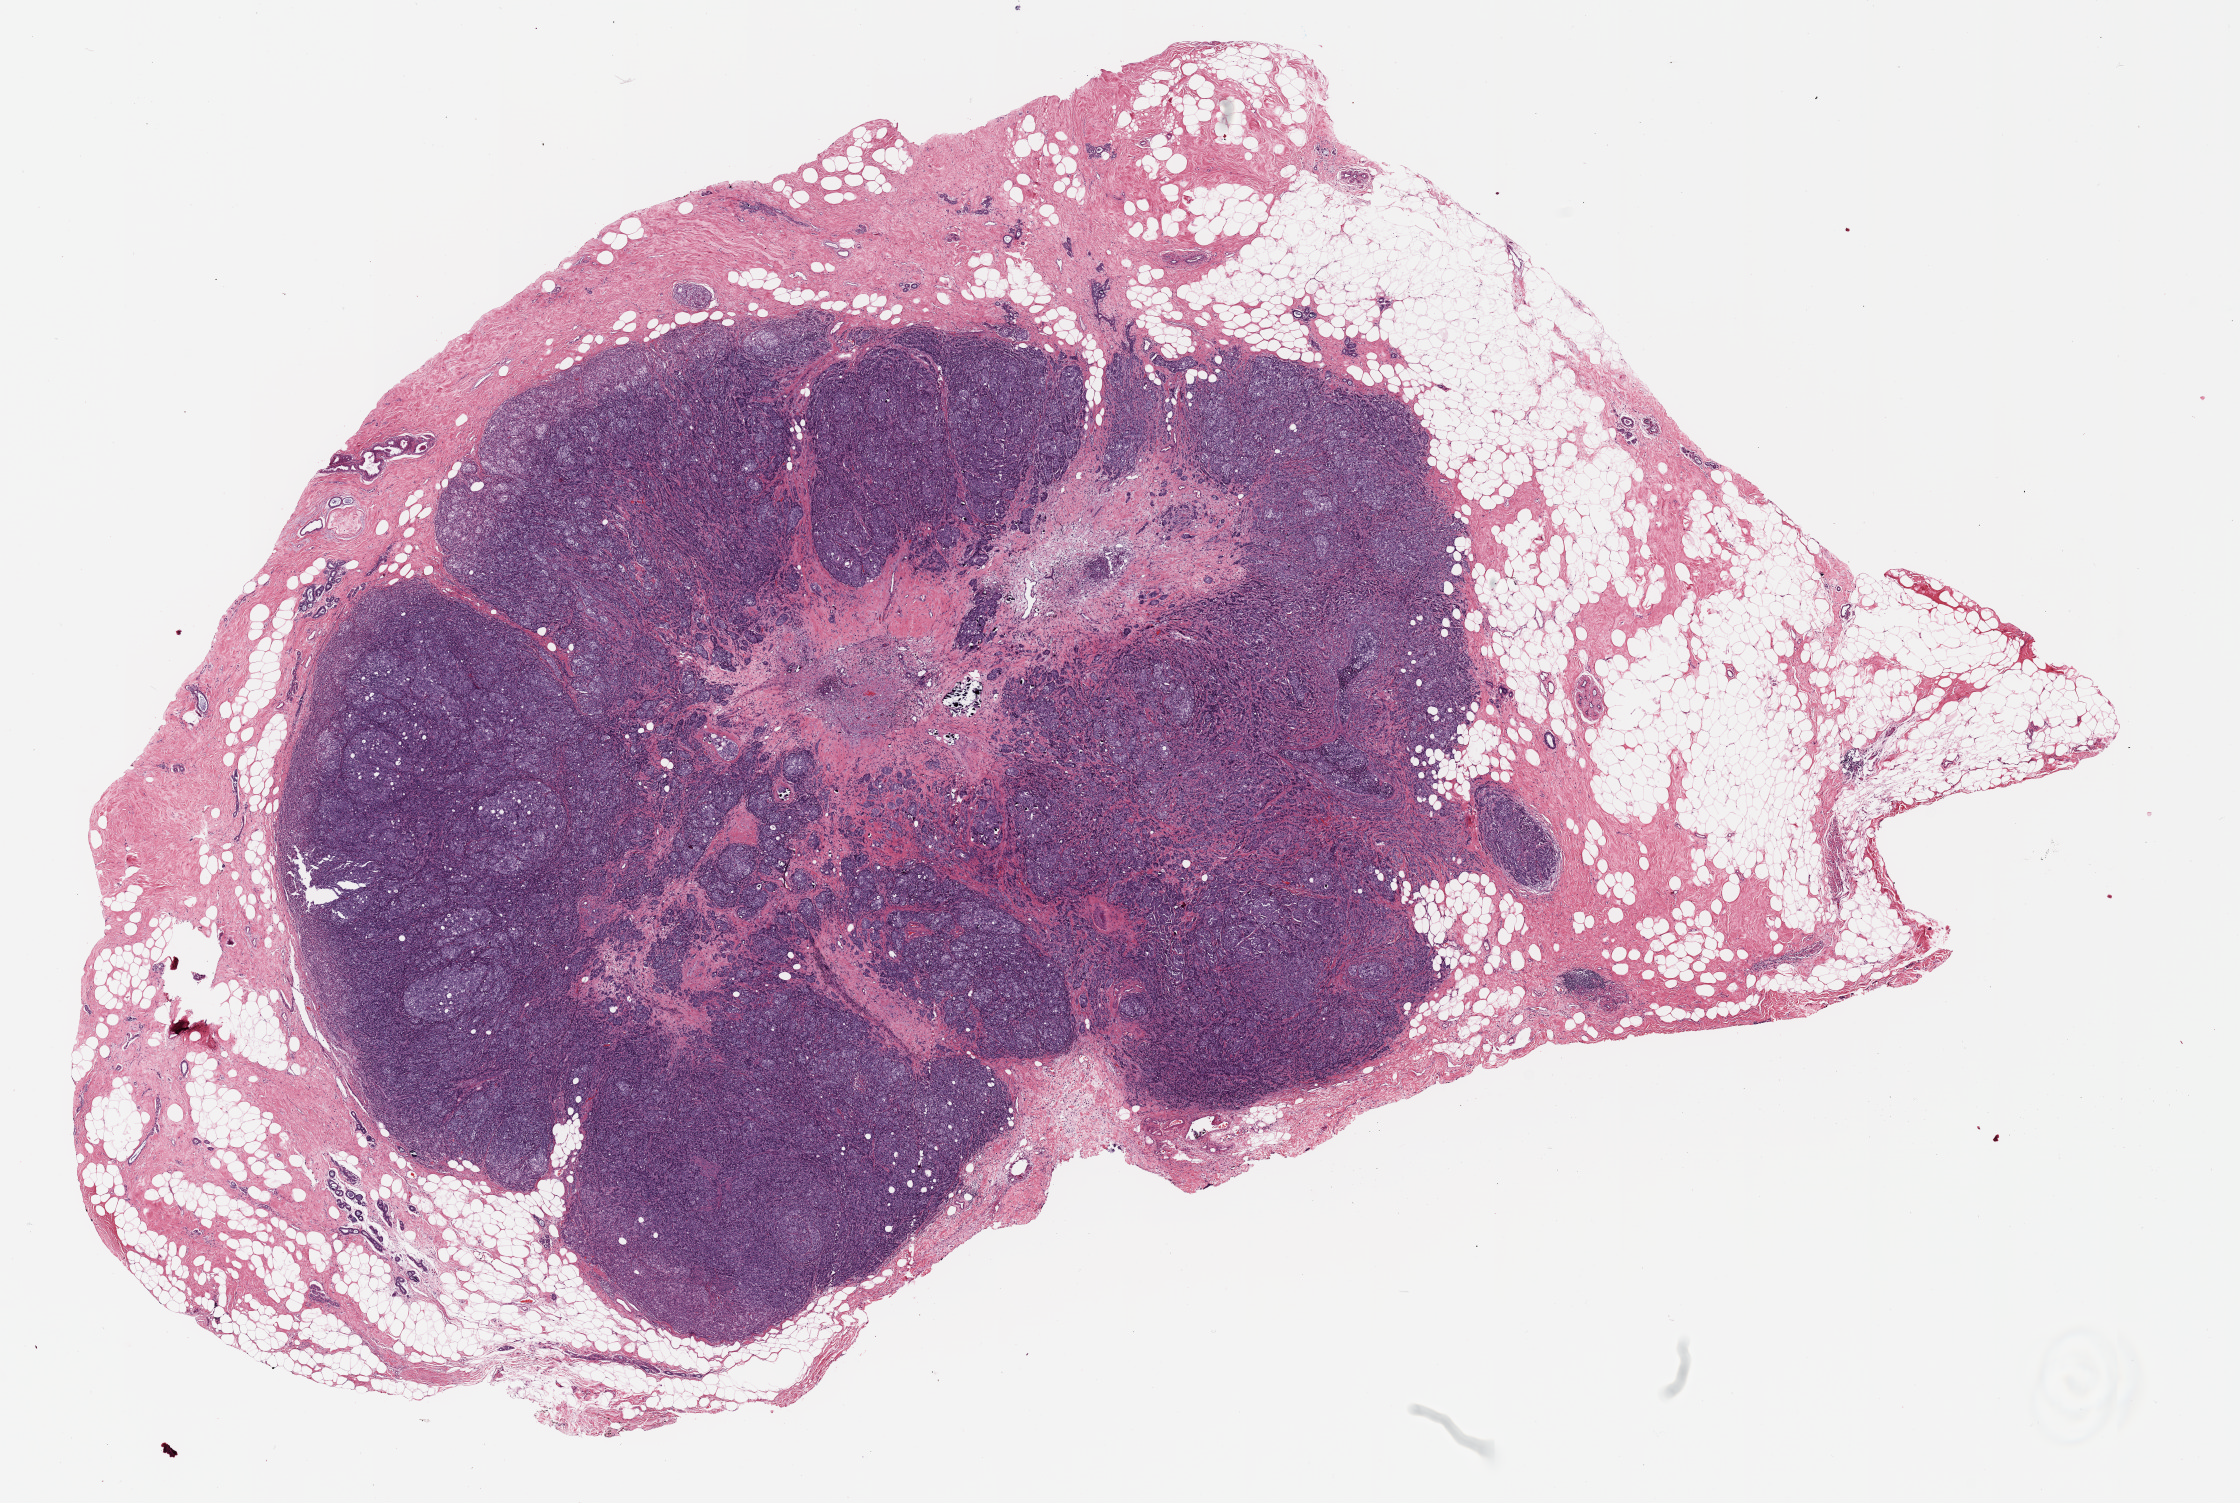
Digitized Hematoxylin and eosin (H&E) stained tissue section (whole slide) — whole scanned area (about 17.9 x 12.0 mm, acquisition: 20x scan) shown as a low-resolution overview, FFPE section, breast, primary tumour sample. Patient: female, age at initial diagnosis 56 years.
Diagnosis: Infiltrating duct carcinoma, NOS.